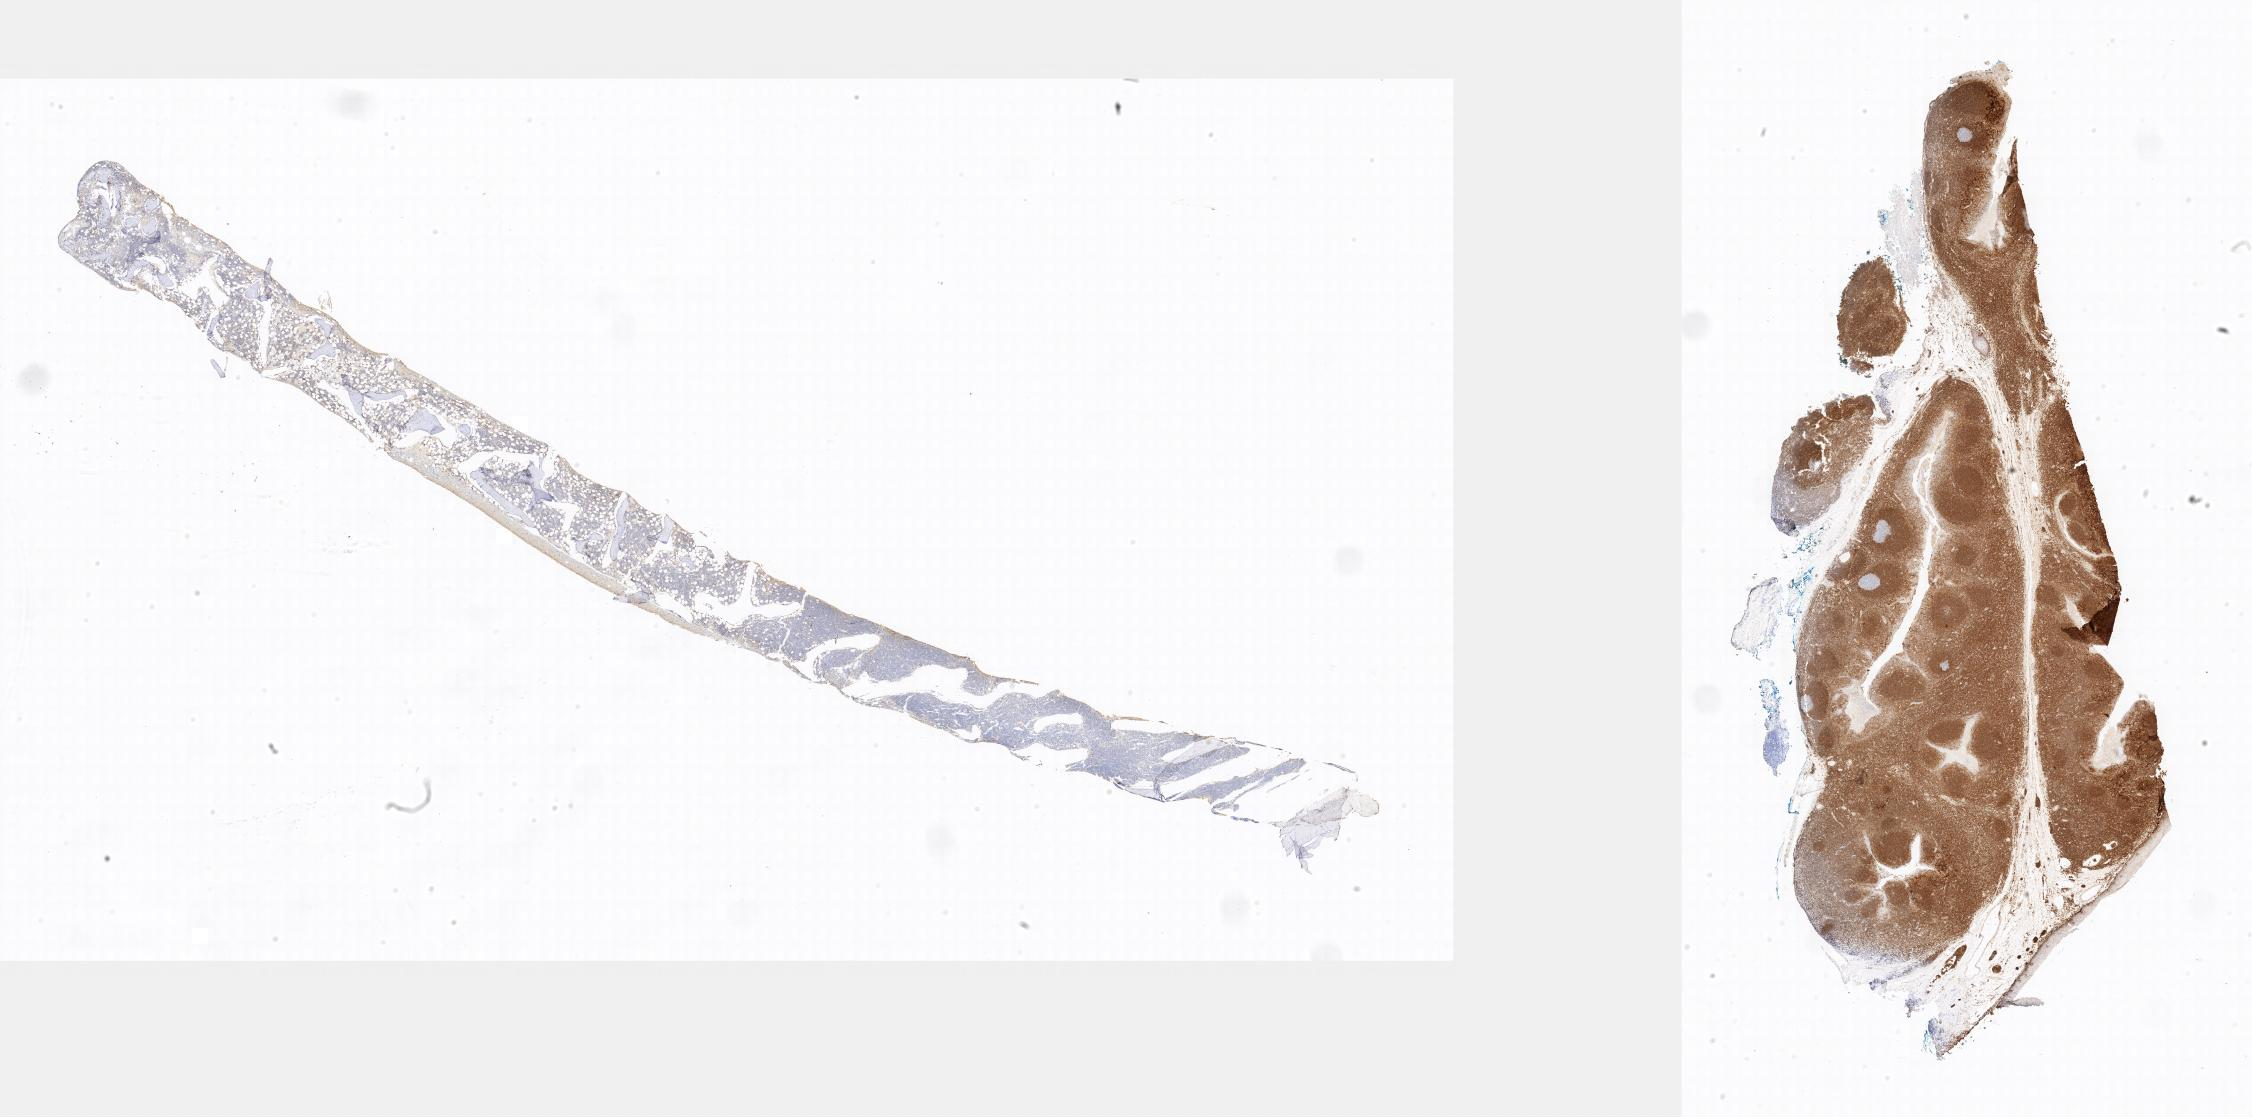
Immunohistochemistry (IHC) whole-slide image stained for BCL2 — whole scanned area shown as a low-resolution overview, tumor tissue. Male patient, 12 years old.
- histologic diagnosis: Burkitt lymphoma, NOS